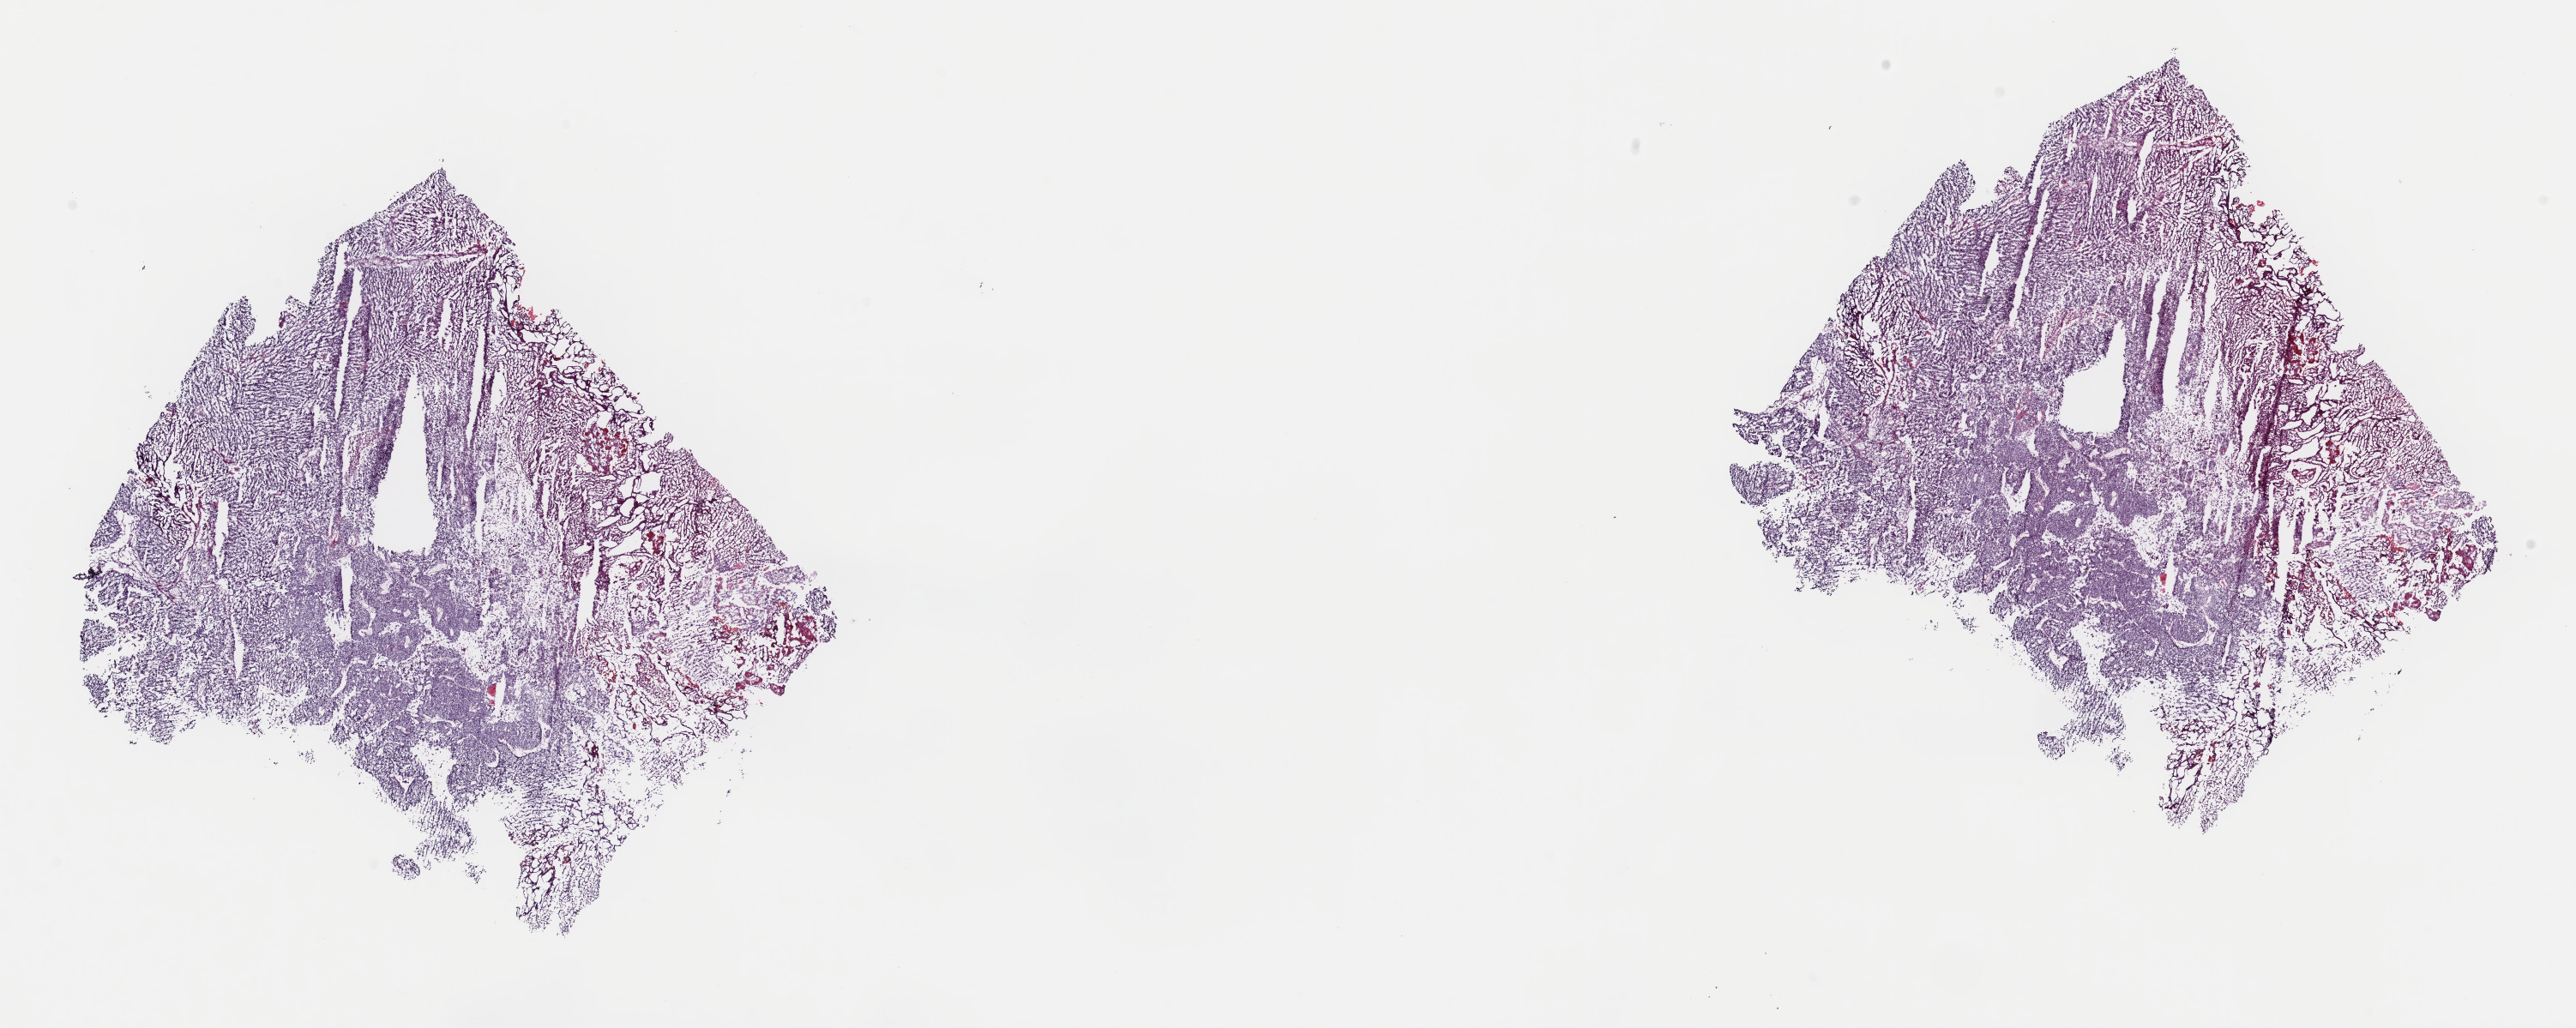
H&E-stained whole-slide image, whole scanned area (about 23.7 x 9.5 mm, acquisition: 40x scan) shown as a low-resolution overview. Frozen section from the top of the tissue portion. Bladder, primary tumour sample. Male patient; age at initial diagnosis 56 years. Histologic grade: high grade. Pathologist review of this section (percent, as recorded): tumour cells 65%, tumour nuclei 65%, normal cells 0%, stromal cells 33%, necrosis 2%. Infiltration values recorded for this section: lymphocyte infiltration 9%, monocyte infiltration 2%, neutrophil infiltration 5%.
AJCC pathologic stage: II (7th edition). Pathologic diagnosis: Transitional cell carcinoma.